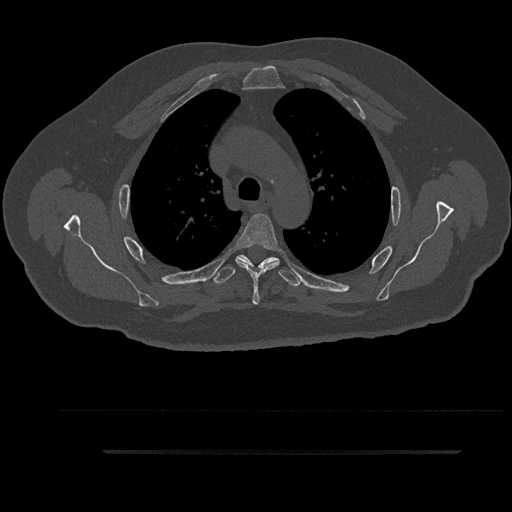
CT including the spine, one axial slice; position 658 of 797 along the scan axis; reconstruction kernel Br40s/3; 120 kVp; bone window (W 1800 / L 400 HU); 0.5 mm slice thickness; 512 × 512 image matrix, field of view 432 × 432 mm. Patient: male, 63 years. Case-level facts recorded for this patient, not image findings: primary cancer: renal; vertebrae with lytic lesions (as recorded): T8.
Outlined on this slice (semi-automatically segmented with operator editing):
- T3 vertebra: bounding box [x1, y1, x2, y2] px = [224, 271, 299, 282]
- T4 vertebra: [236, 214, 280, 305]
- T5 vertebra: [213, 254, 300, 288]